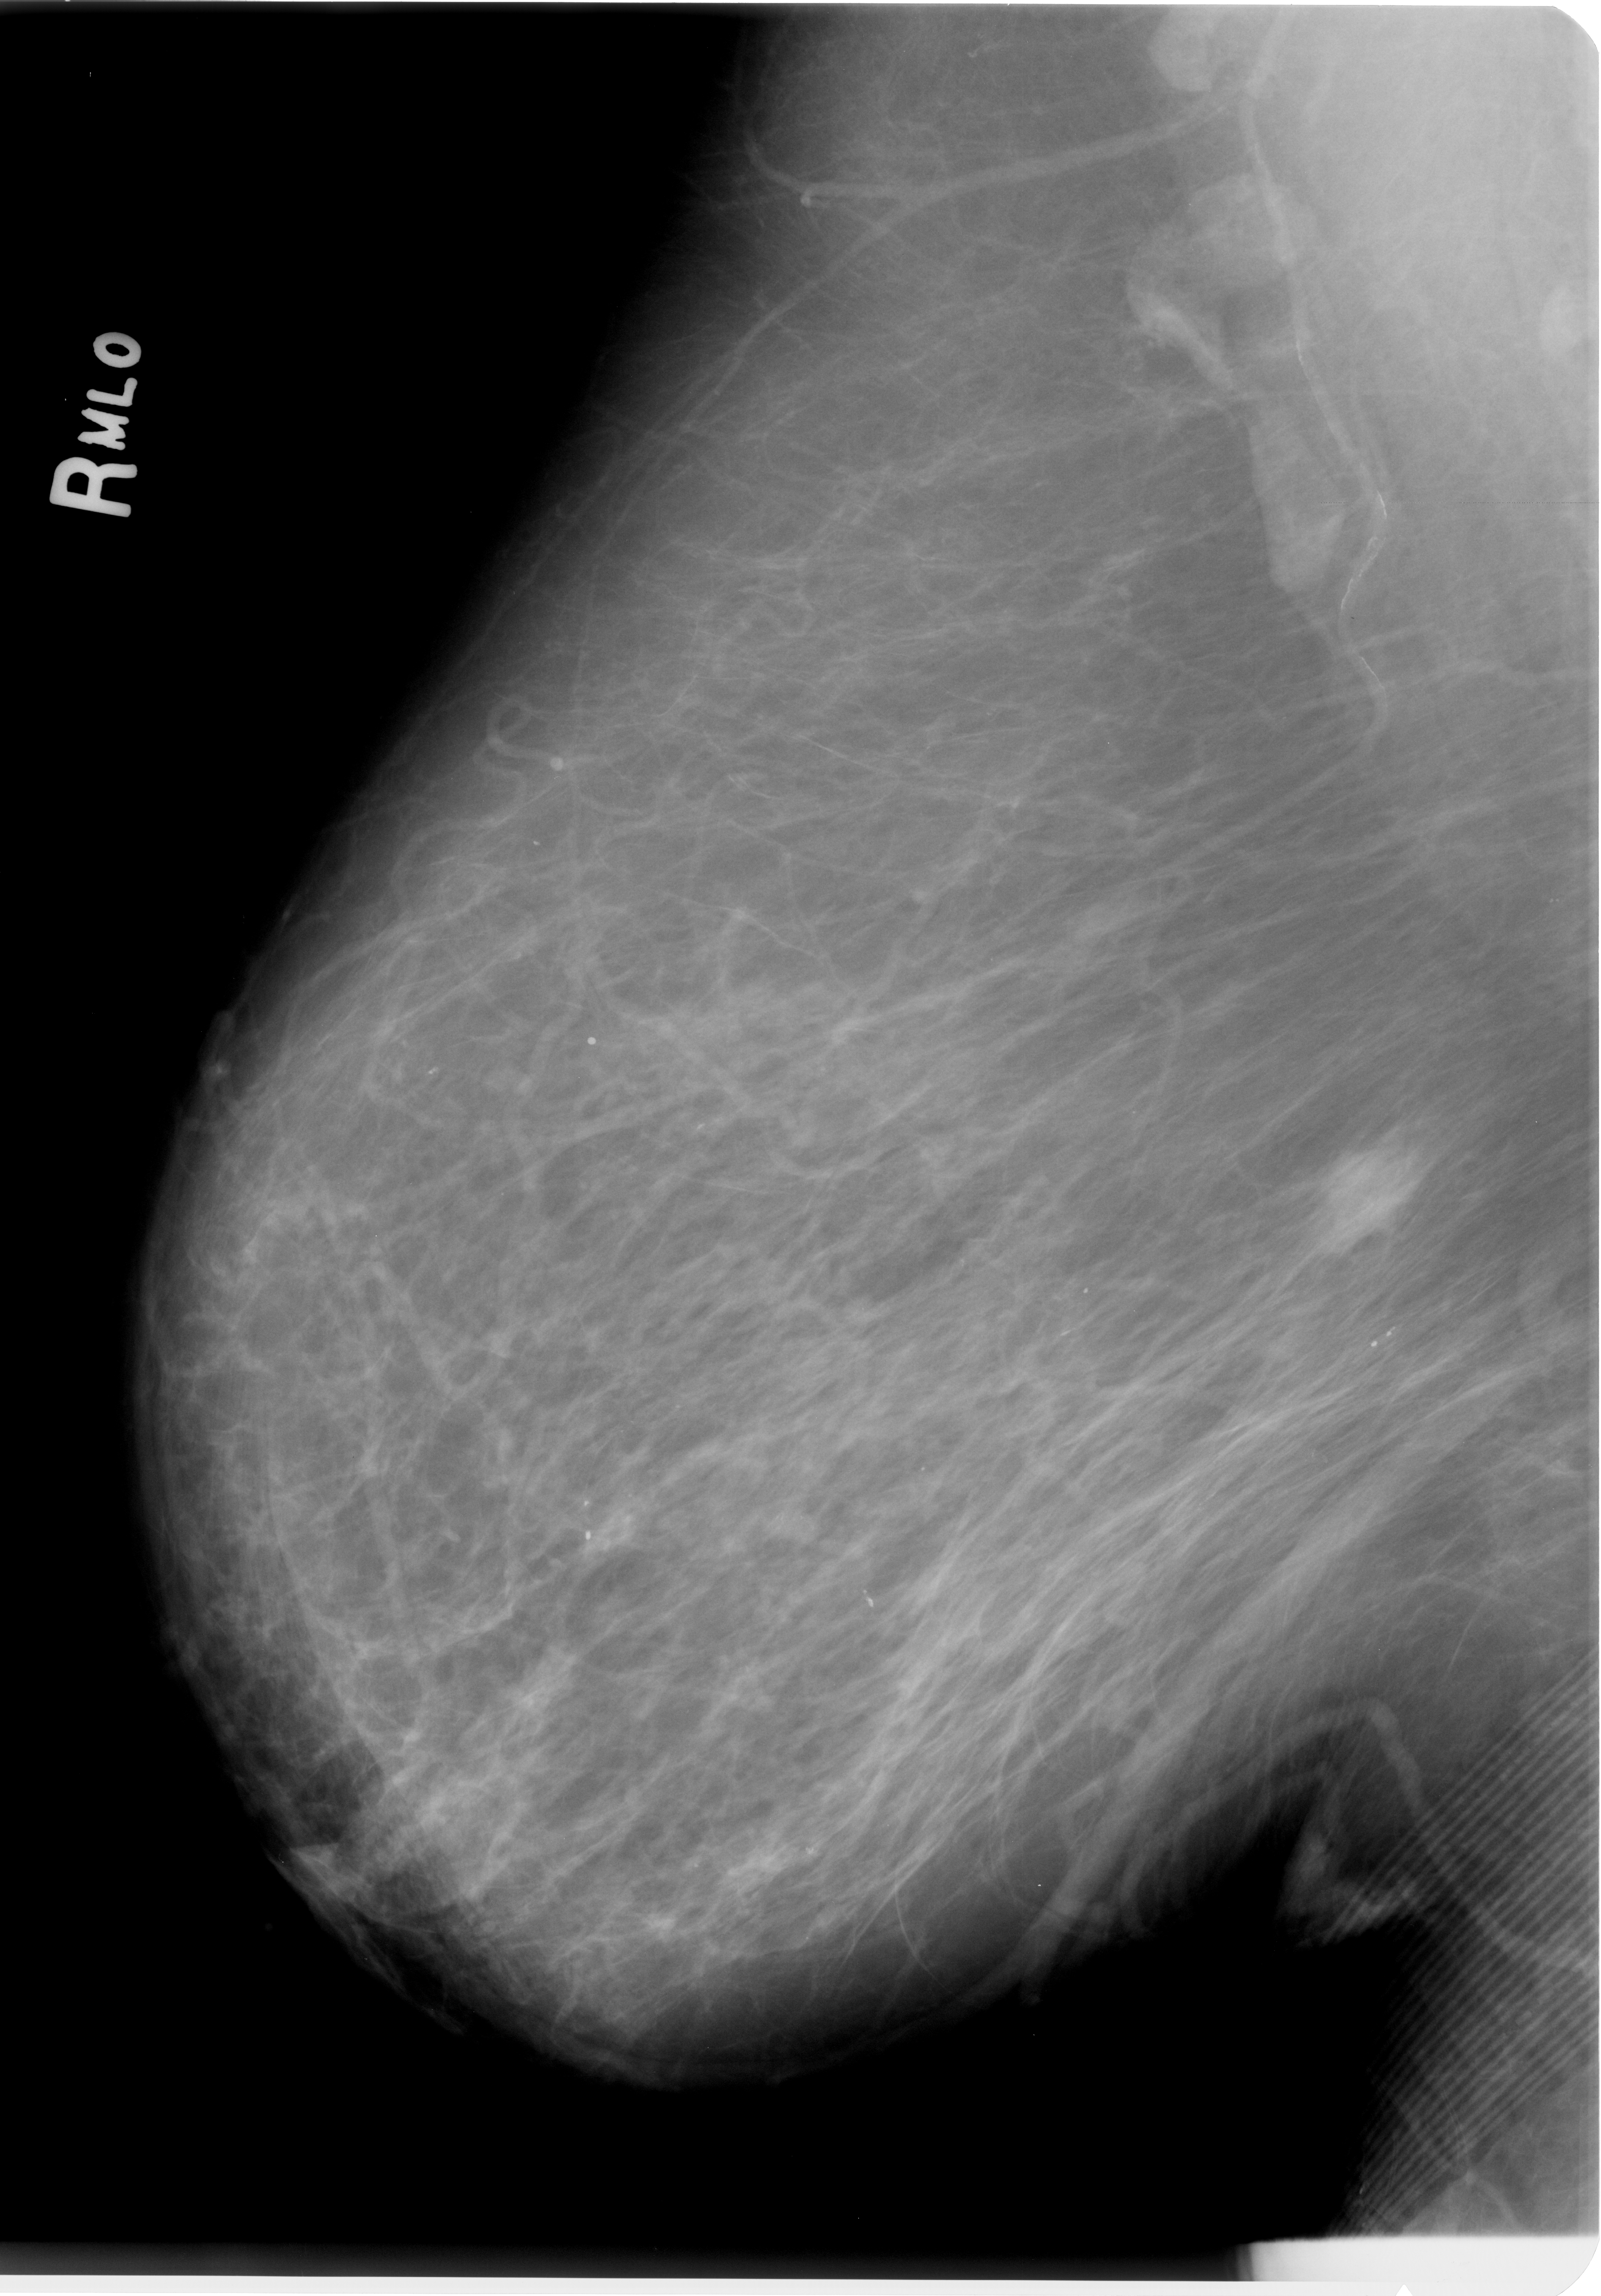
Digitized screen-film mammogram. Right breast. Mediolateral oblique (MLO) view. BI-RADS breast density category 2 (scale 1–4). 1601 × 2296 image matrix.
Expert-marked regions of interest on this image (one box per marked abnormality):
- mass, shape irregular, margins spiculated; BI-RADS assessment category 4; pathology (as recorded): malignant: bounding box (x1, y1, x2, y2) in pixels: (1316, 1135, 1420, 1238)